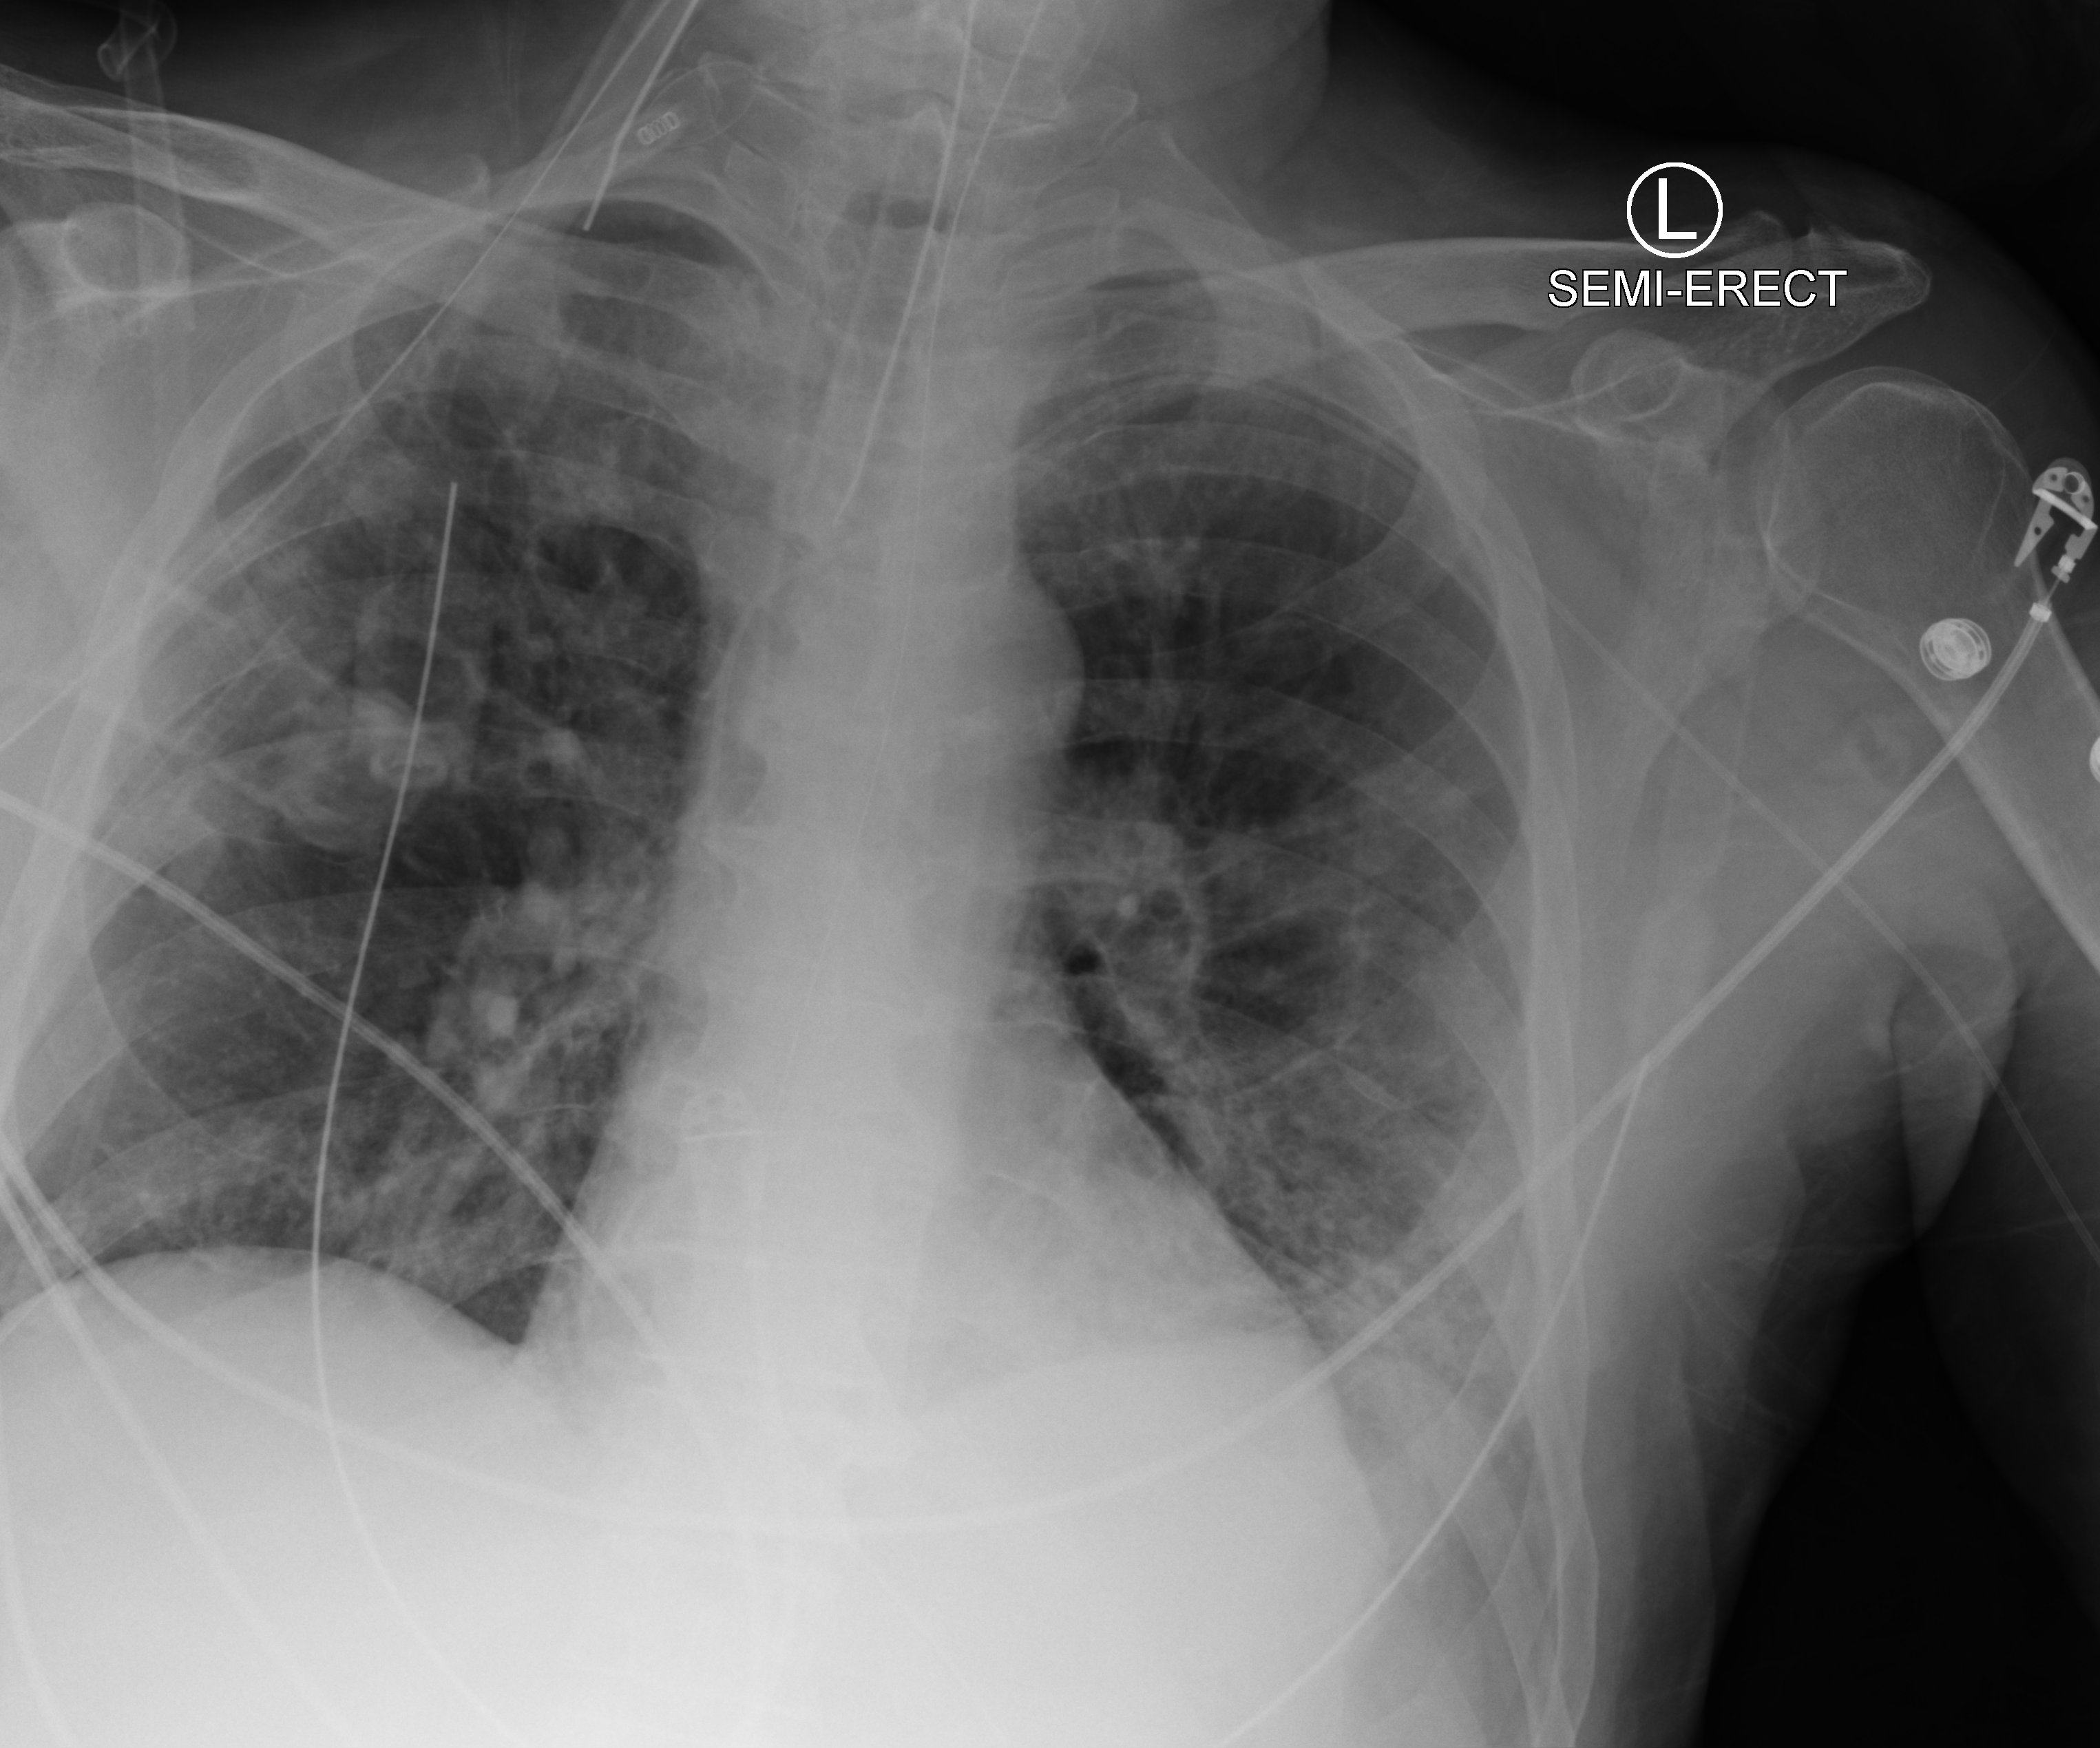
Portable chest radiograph; anteroposterior (AP) projection. Male patient hospitalised with COVID-19, age 60–74 years.
Hospital-stay facts (about this admission, not read from this image; timing relative to this image not recorded):
- mechanically ventilated during this hospital stay: yes
- smoking status (admission record): never